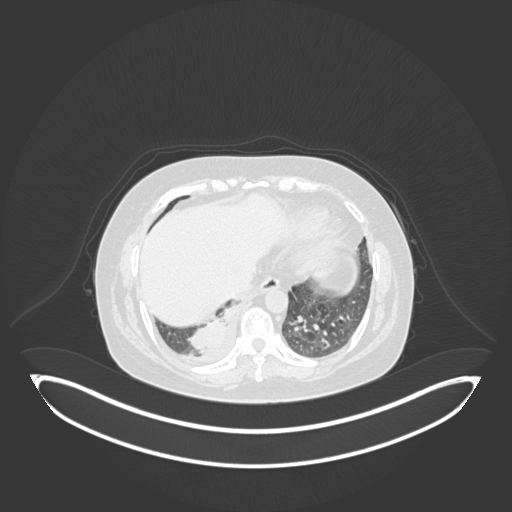
Chest CT, one axial slice; slice 31 of 231 in the series (ordered by position); reconstruction kernel B30f; 120 kVp; lung window (W 1500 / L -600 HU); 1 mm slice thickness; 512 × 512 image matrix. Patient: female, 56 years. Case-level facts recorded for this patient, not image findings: clinical TNM (as recorded): T2b N1 M0.
Outlined on this slice (bounding box drawn by a radiologist):
- lung tumour (recorded histology: small cell carcinoma): box from (x=184, y=297) to (x=243, y=353) px